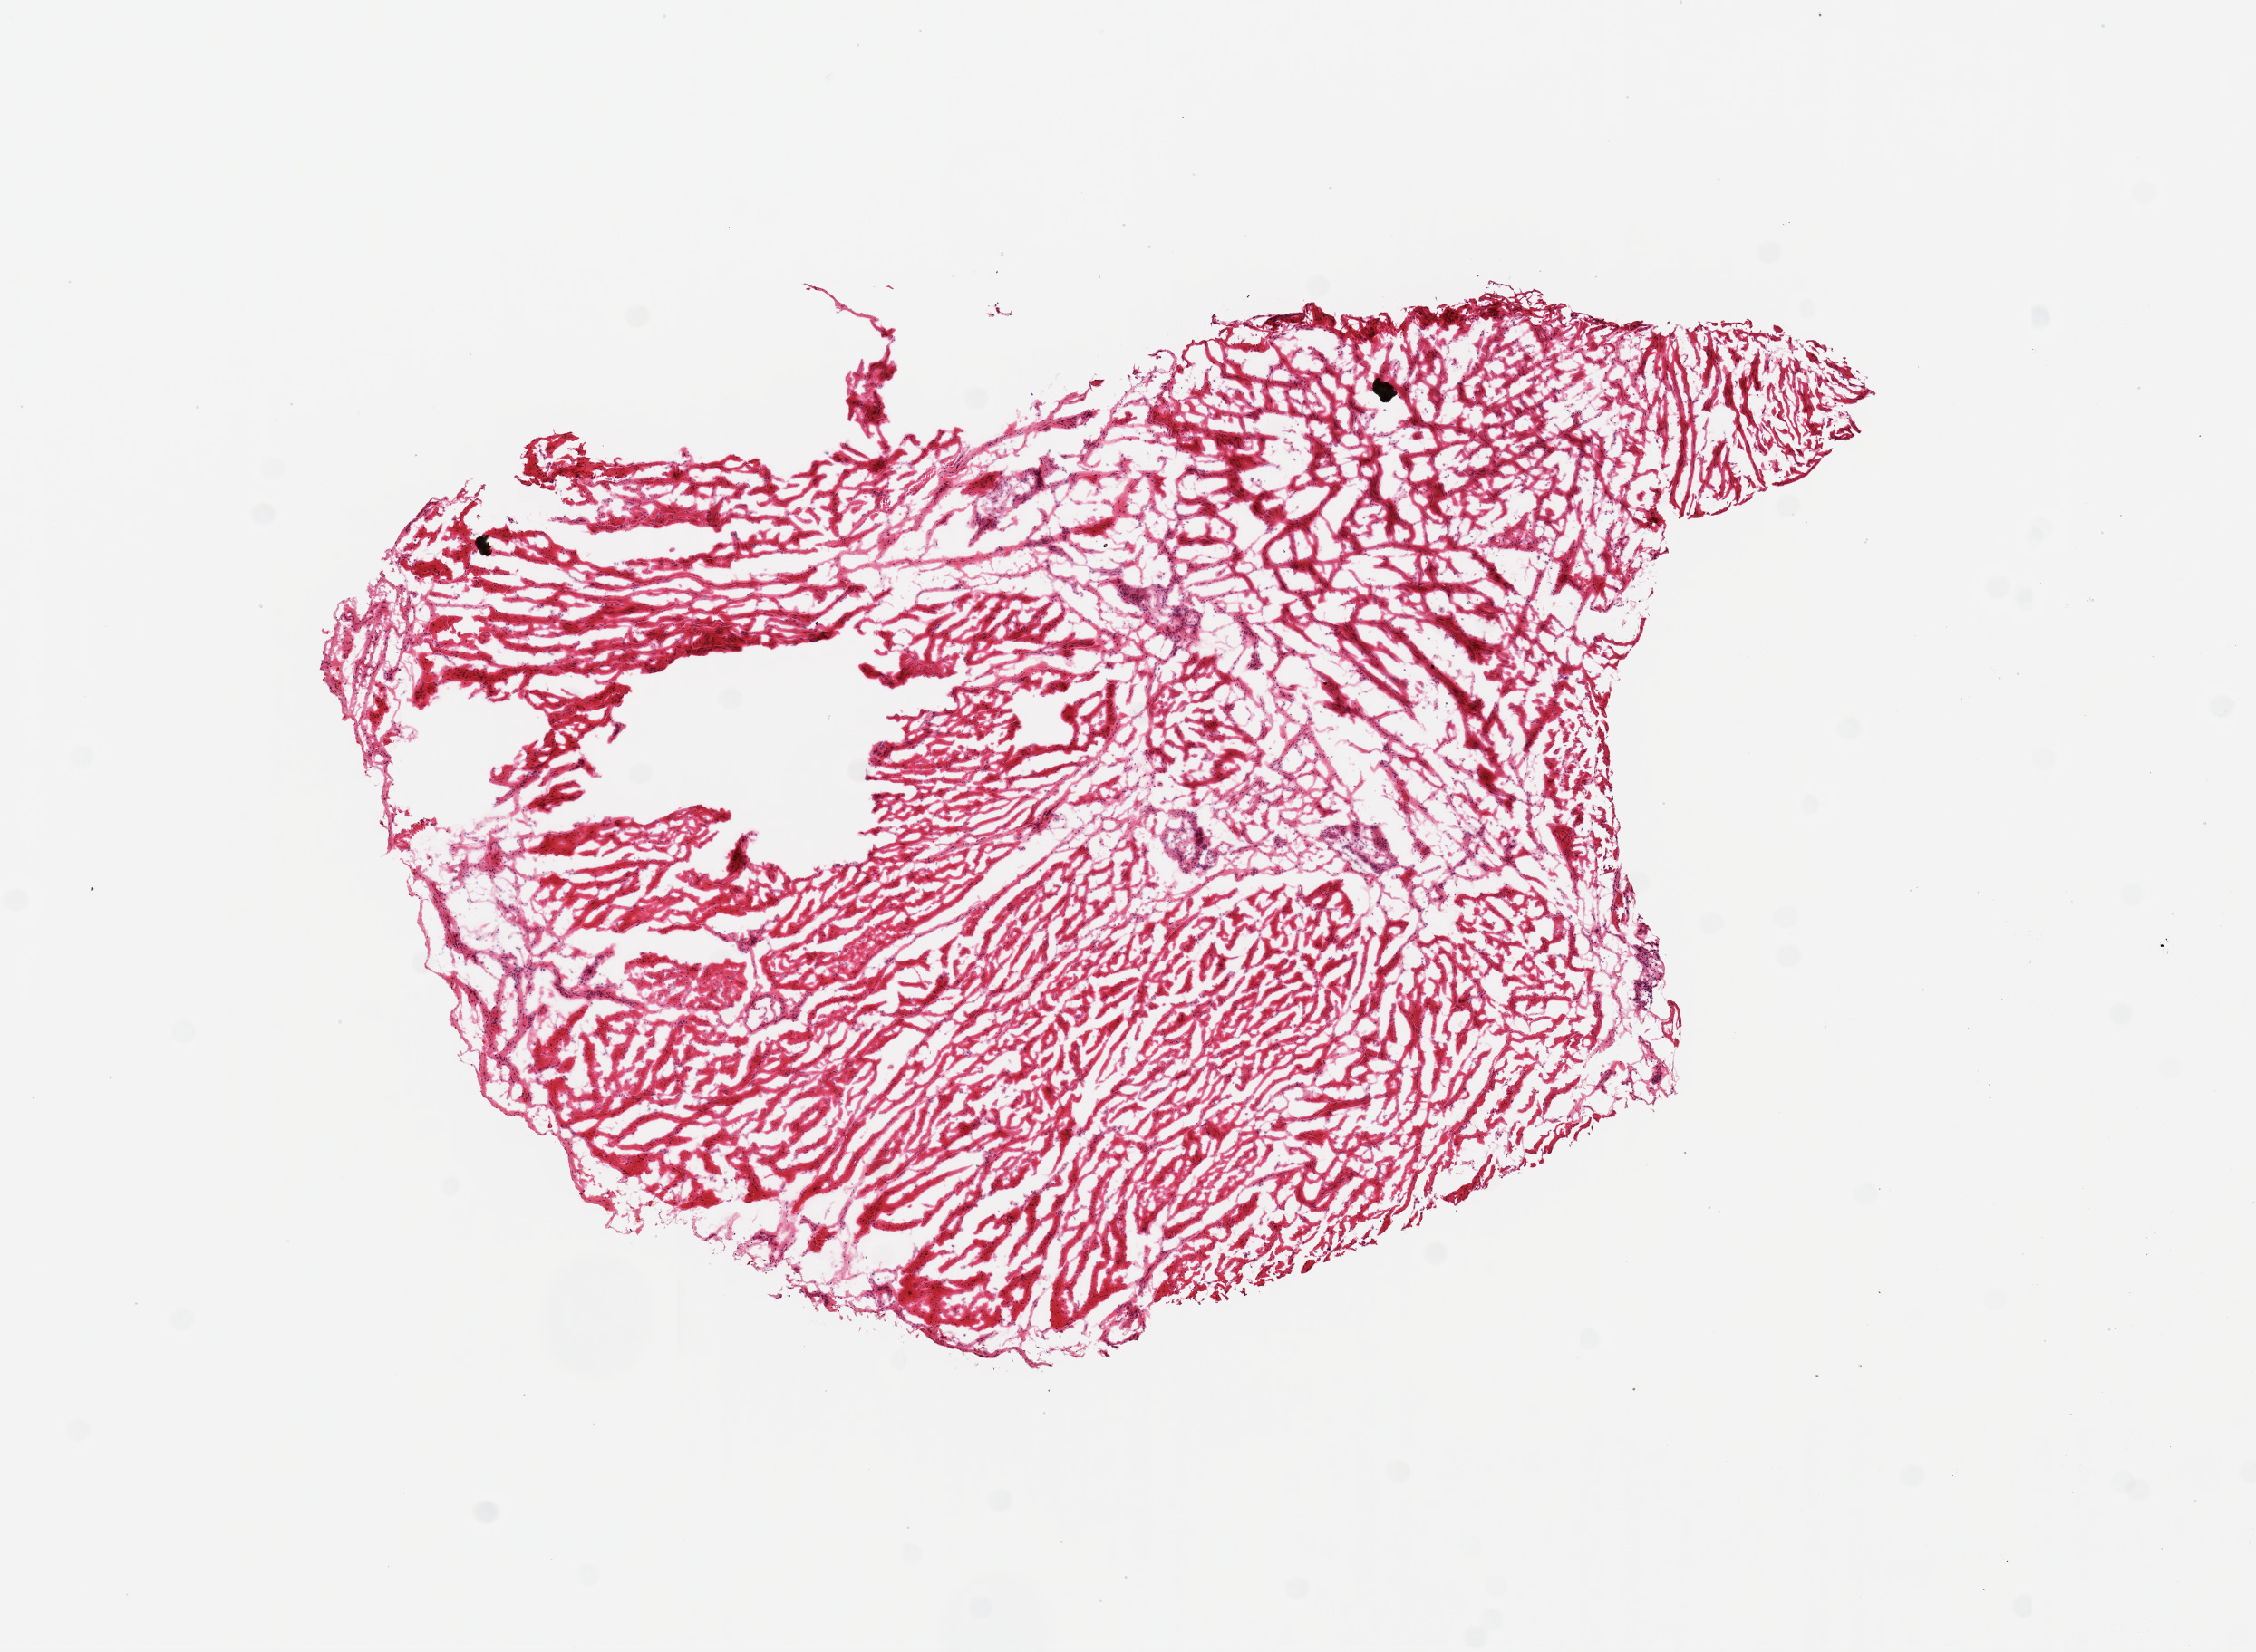
Whole-slide image, H&E stain, brightfield — a low-resolution overview of the entire scanned area, about 9.8 x 7.2 mm. Female donor.
* specimen: frozen section; target tissue: esophageal muscle; tissue donor sample